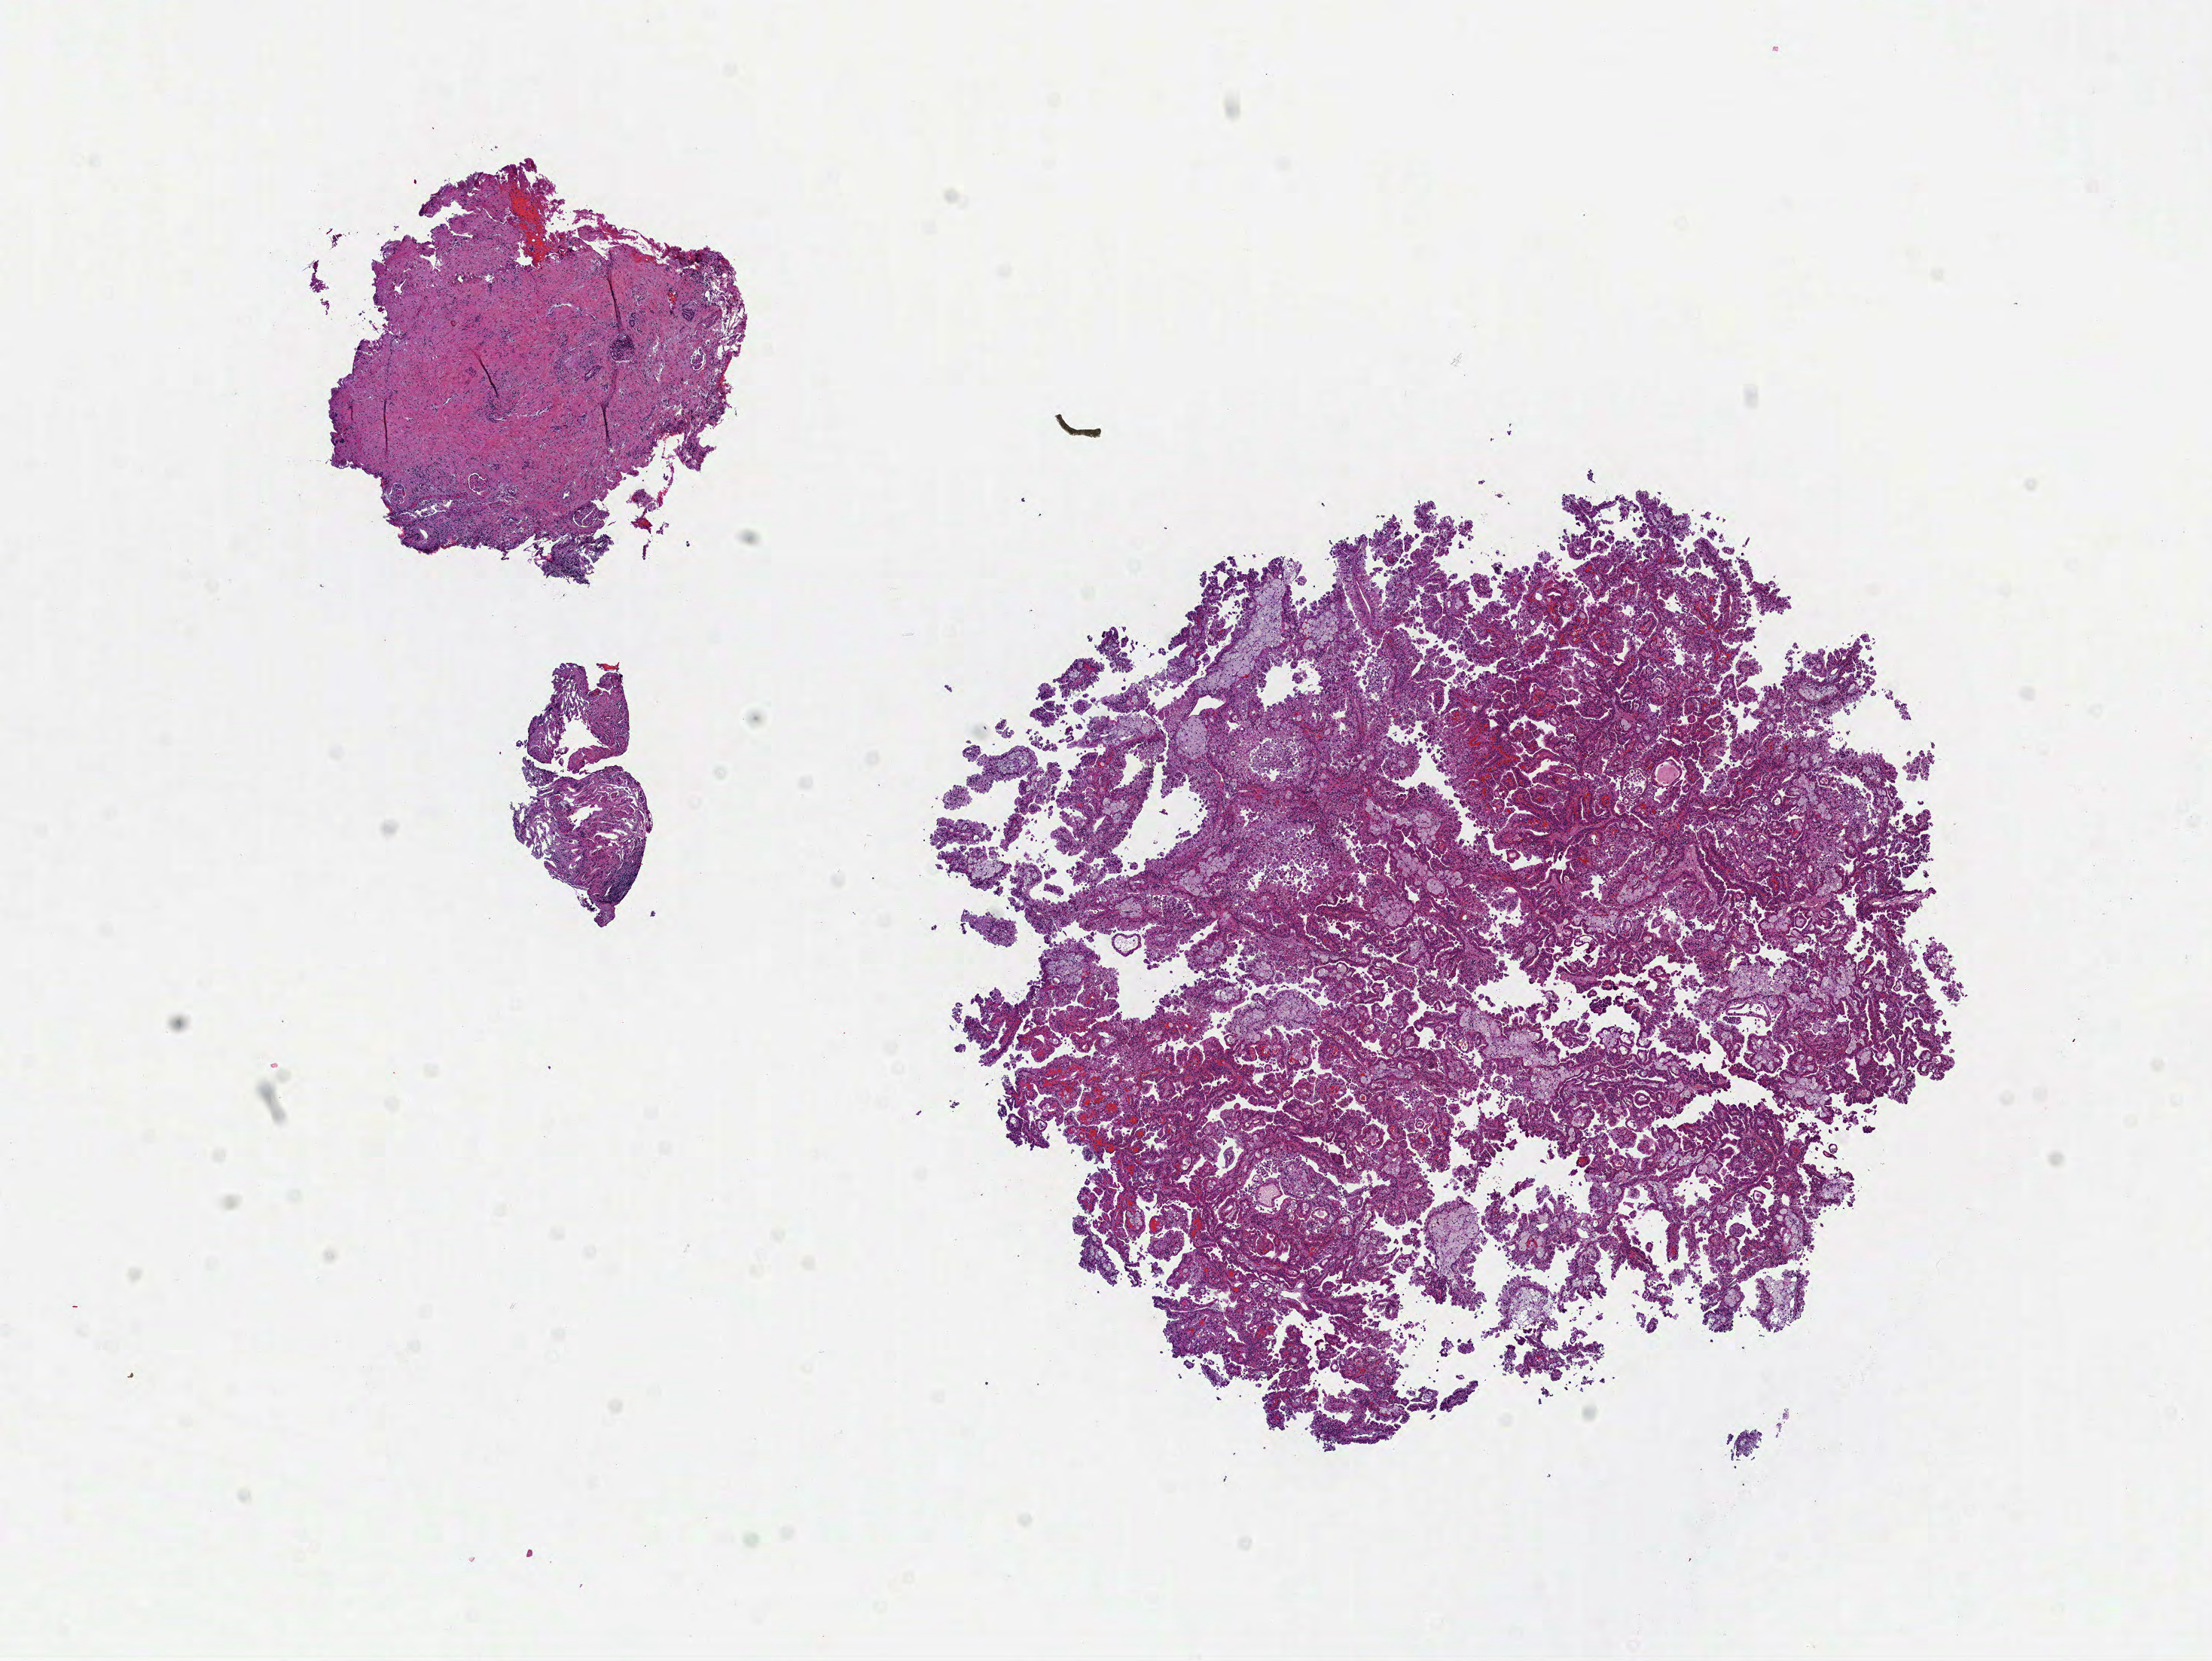
H&E whole-slide image — a low-resolution overview of the entire scanned area, about 11.8 x 8.9 mm, formalin-fixed paraffin-embedded (FFPE) diagnostic section, kidney, primary tumour sample. Male, age 55 years at initial diagnosis.
• pathologic diagnosis: Papillary adenocarcinoma, NOS
• AJCC pathologic stage: I